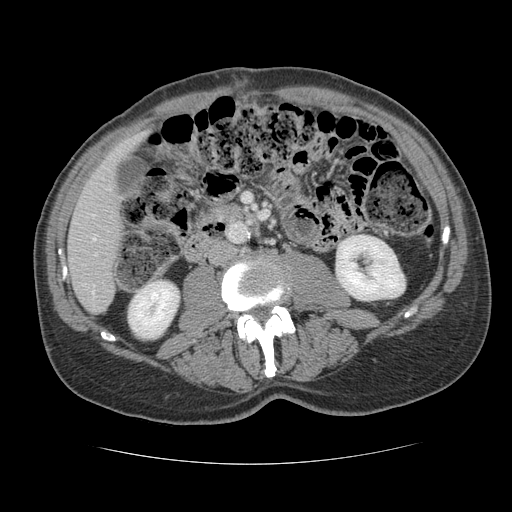
Contrast-enhanced abdominal CT, one axial slice. Slice 39 of 134 in the series (ordered by position). 120 kVp. Soft-tissue window (W 400 / L 40 HU). 2.5 mm slice thickness. 512 × 512 image matrix. Male patient, age 68 years. Case-level facts recorded for this patient, not image findings: diagnosis: colorectal cancer liver metastases, imaged before liver resection; multiple liver metastases: yes; largest metastasis: 2.2 cm; chemotherapy before resection: no.
Annotated regions visible in this slice (outlined manually by an expert reader):
- hepatic veins: bounding box [x1, y1, x2, y2] px = [93, 215, 96, 240]
- liver: [68, 136, 142, 313]
- planned liver remnant (the part of the liver to remain after resection): [68, 135, 142, 313]
- portal vein (with intrahepatic branches): [92, 291, 94, 294]